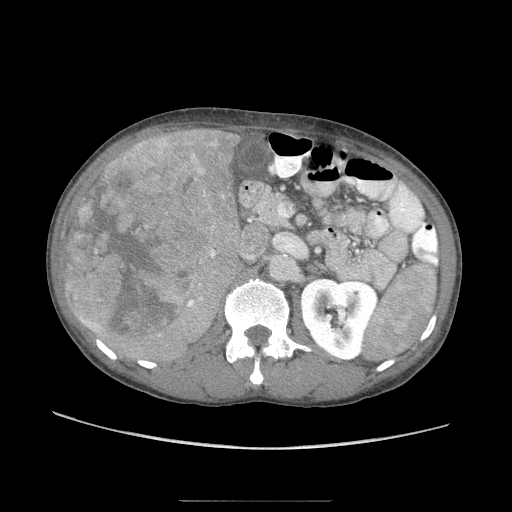
Contrast-enhanced abdominal CT (liver protocol), one axial slice. Slice 38 of 103 in the series (ordered by position). 120 kVp. Soft-tissue window (W 400 / L 40 HU). 2.5 mm slice thickness. 512 × 512 image matrix, field of view 380 × 380 mm. Case-level facts recorded for this patient, not image findings: diagnosis: hepatocellular carcinoma (patient treated with transarterial chemoembolisation; whether this scan precedes or follows treatment is not stated here); TNM stage (as recorded): Stage-IIIA; Child-Pugh class: A; tumour differentiation: moderately differentiated; tumour nodularity: multinodular.
Structures marked on this image (semi-automatic segmentation, software-assisted and operator-edited):
- liver parenchyma outside the tumour (the mass and vessels are separate outlines, so this box may not span the whole liver): box from (x=64, y=126) to (x=256, y=362) px
- mass: (x=63, y=136)–(x=220, y=345)
- liver vessels: (x=83, y=142)–(x=213, y=326)